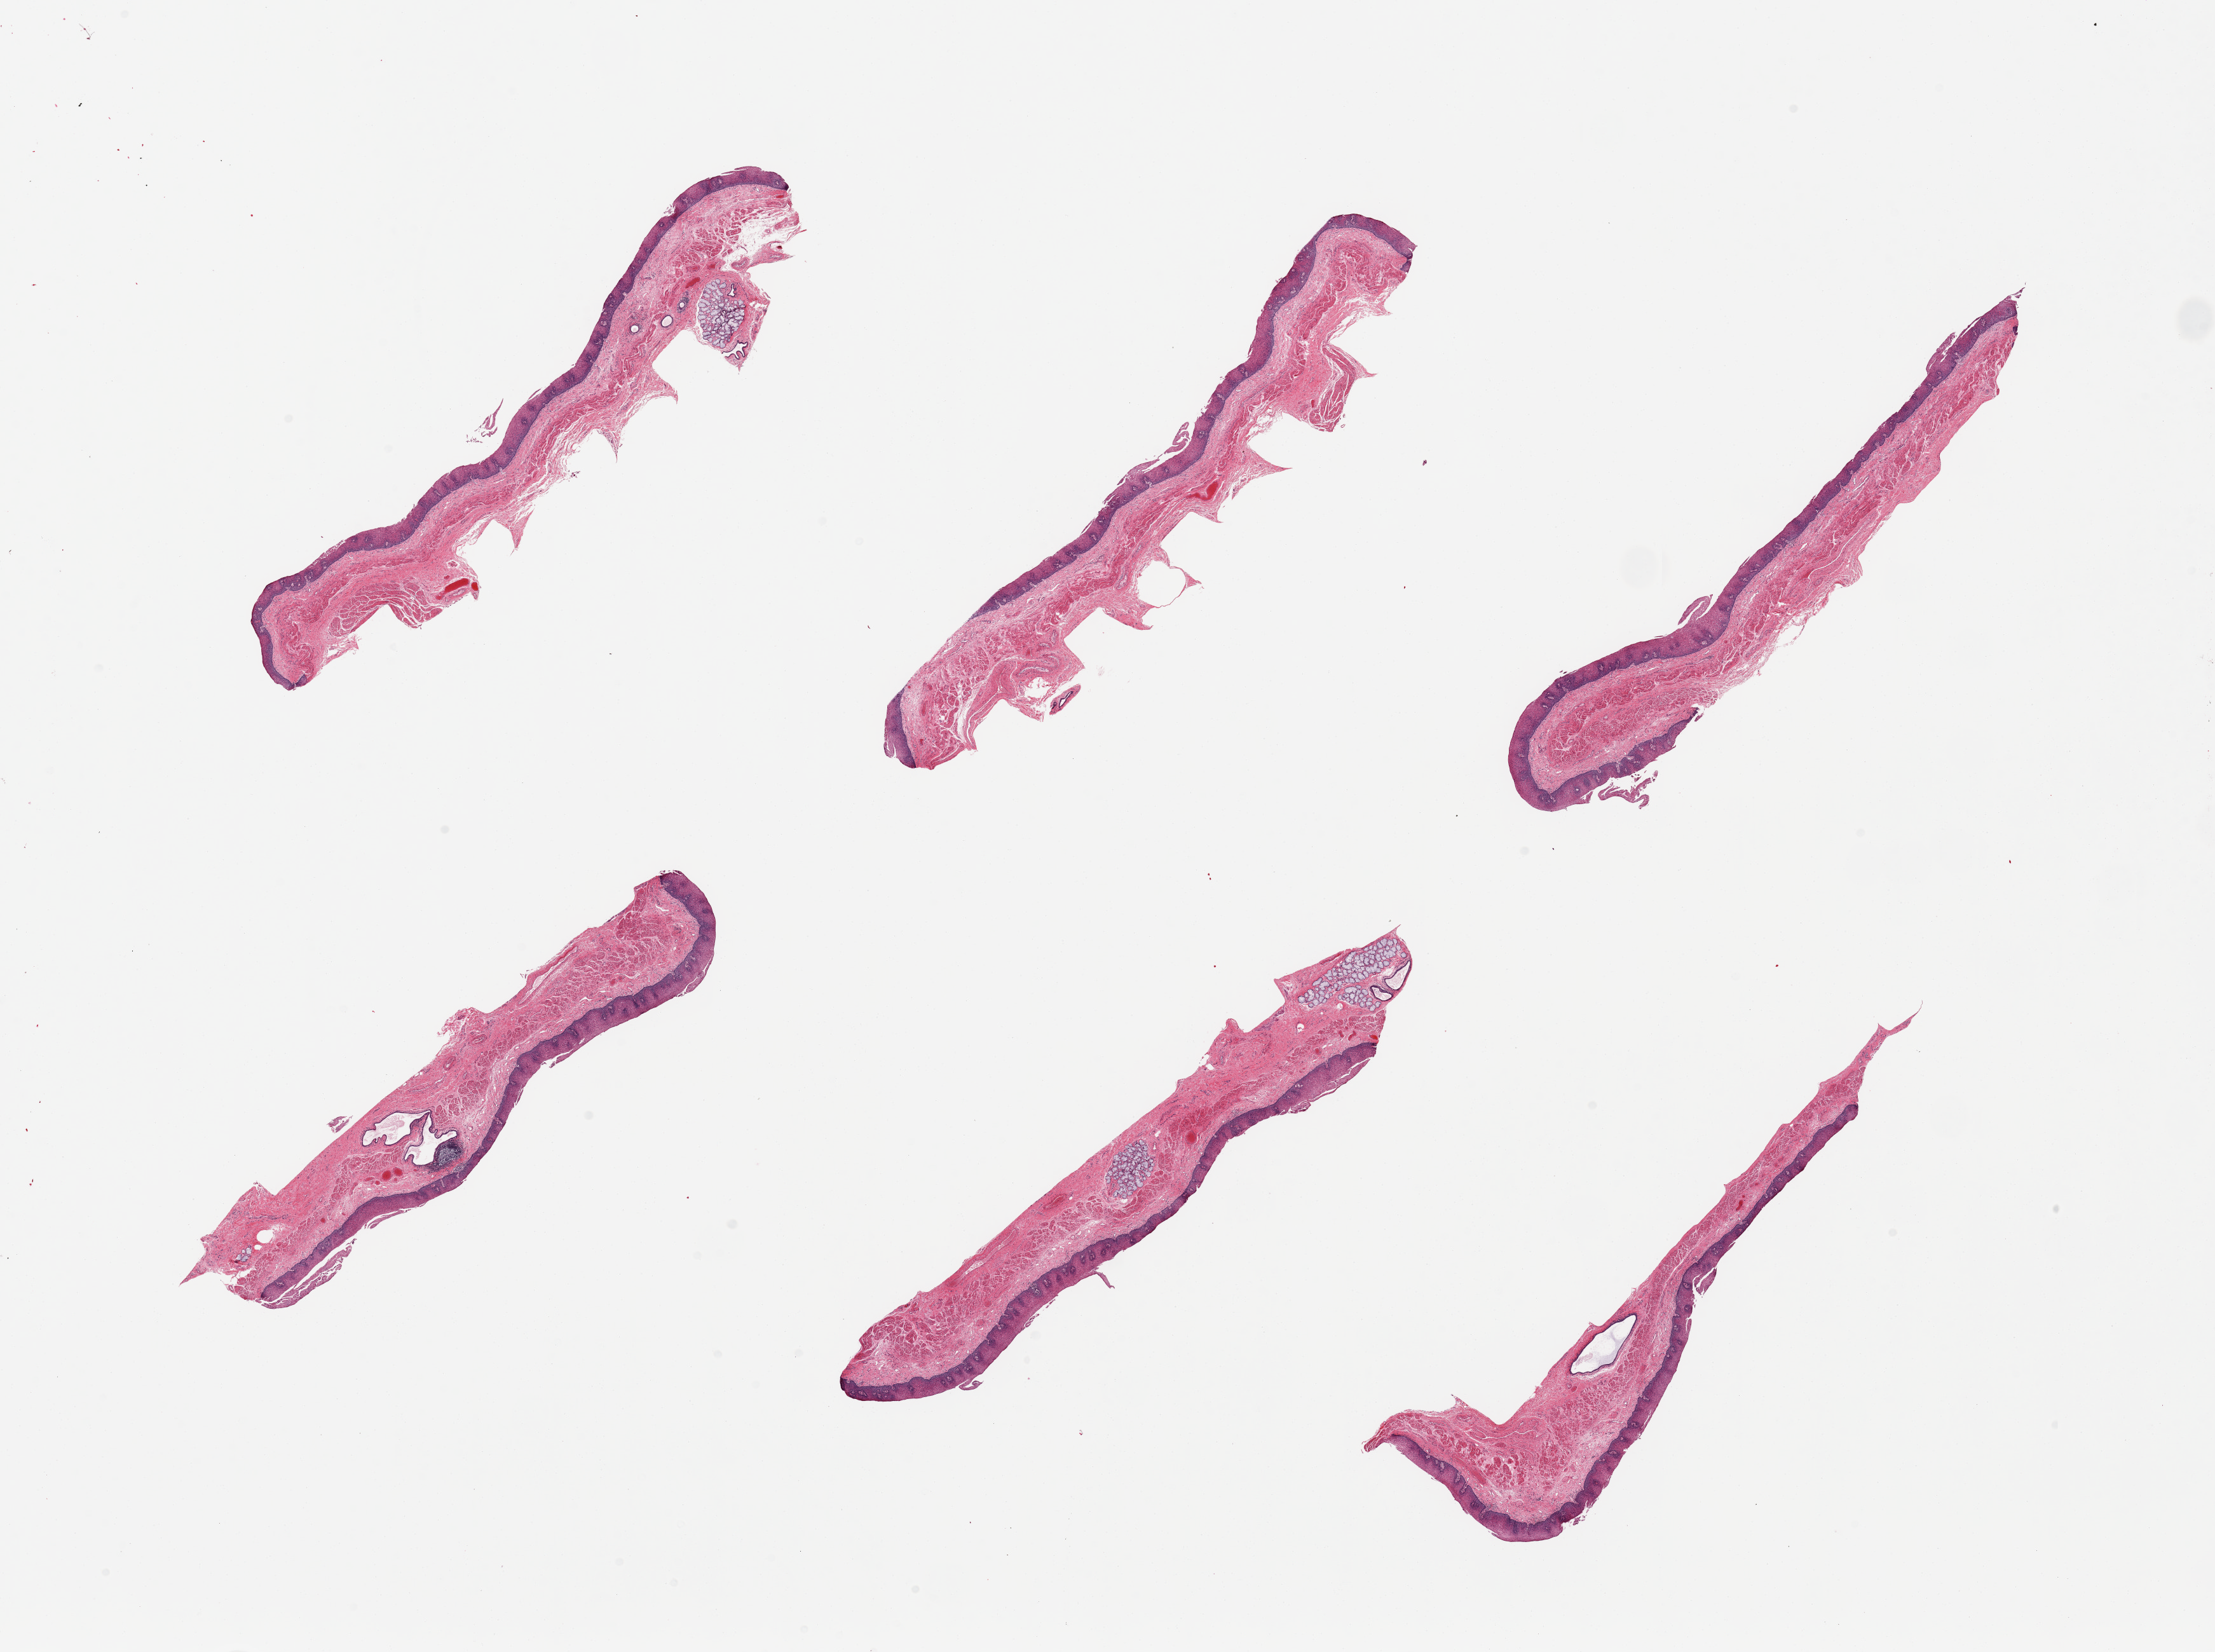
Haematoxylin and eosin whole-slide image, brightfield — a low-resolution overview of the entire scanned area, about 27.6 x 20.6 mm (slide scanned at 20x); PAXgene-fixed, paraffin-embedded tissue; sampled site (target tissue): esophageal mucous membrane; tissue donor sample. Donor: male.
Pathologist's review note for this sample: 6 pieces; pseudodiverticulosis; few pieces include small portion of muscularis propria.